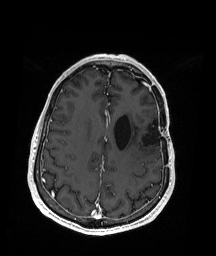
Brain MRI from a brain-tumour surgery series, one axial slice. Position 64 of 192 along the scan axis. T1-weighted post-contrast. 1 mm slice thickness. 216 × 256 image matrix, field of view 211 × 250 mm. From the clinical record (not read from this slice): histopathology: Oligodendroglioma; WHO grade: 2.
Annotated regions visible in this slice (manually delineated by an expert):
- previous resection cavity: box from (x=132, y=123) to (x=156, y=146) px